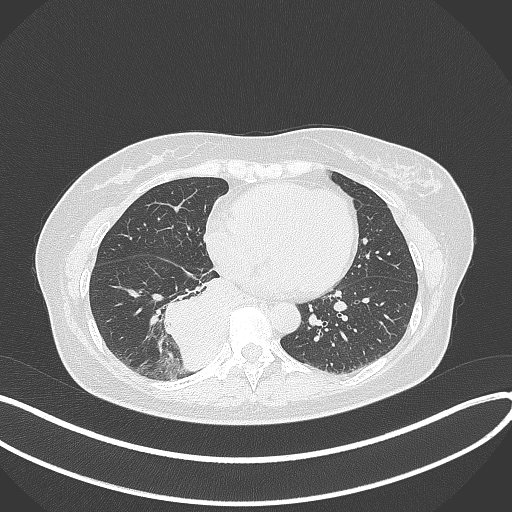
Chest CT, one axial slice. Slice 132 of 331 in the series (ordered by position). Reconstruction kernel B70f. 120 kVp. Lung window (W 1500 / L -600 HU). 512 × 512 image matrix, field of view 400 × 400 mm. Female patient, age 54 years. From the clinical record (not read from this slice): clinical TNM (as recorded): T4 N0 M0.
Outlined on this slice (bounding box drawn by a radiologist):
- lung tumour (recorded histology: adenocarcinoma): bounding box (x1, y1, x2, y2) in pixels: (157, 271, 255, 367)